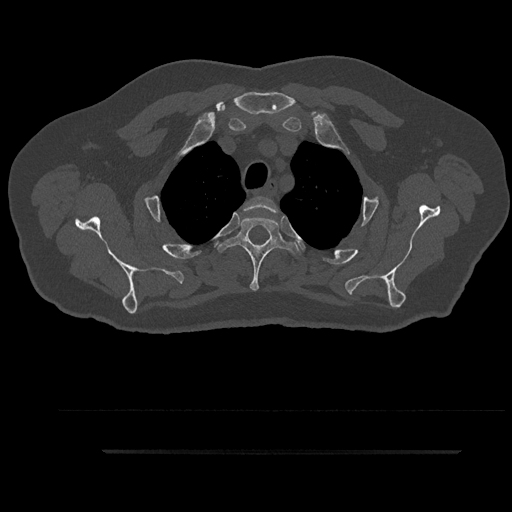
CT including the spine, one axial slice; position 722 of 797 along the scan axis; bone window (W 1800 / L 400 HU); 0.5 mm slice thickness; 512 × 512 image matrix, field of view 432 × 432 mm. Male patient, age 63 years. Case-level facts recorded for this patient, not image findings: primary cancer: renal; vertebrae with lytic lesions (as recorded): T8.
Outlined on this slice (semi-automatically segmented with operator editing):
- T2 vertebra: bounding box (x1, y1, x2, y2) in pixels: (244, 196, 278, 212)
- T3 vertebra: (218, 216, 300, 291)